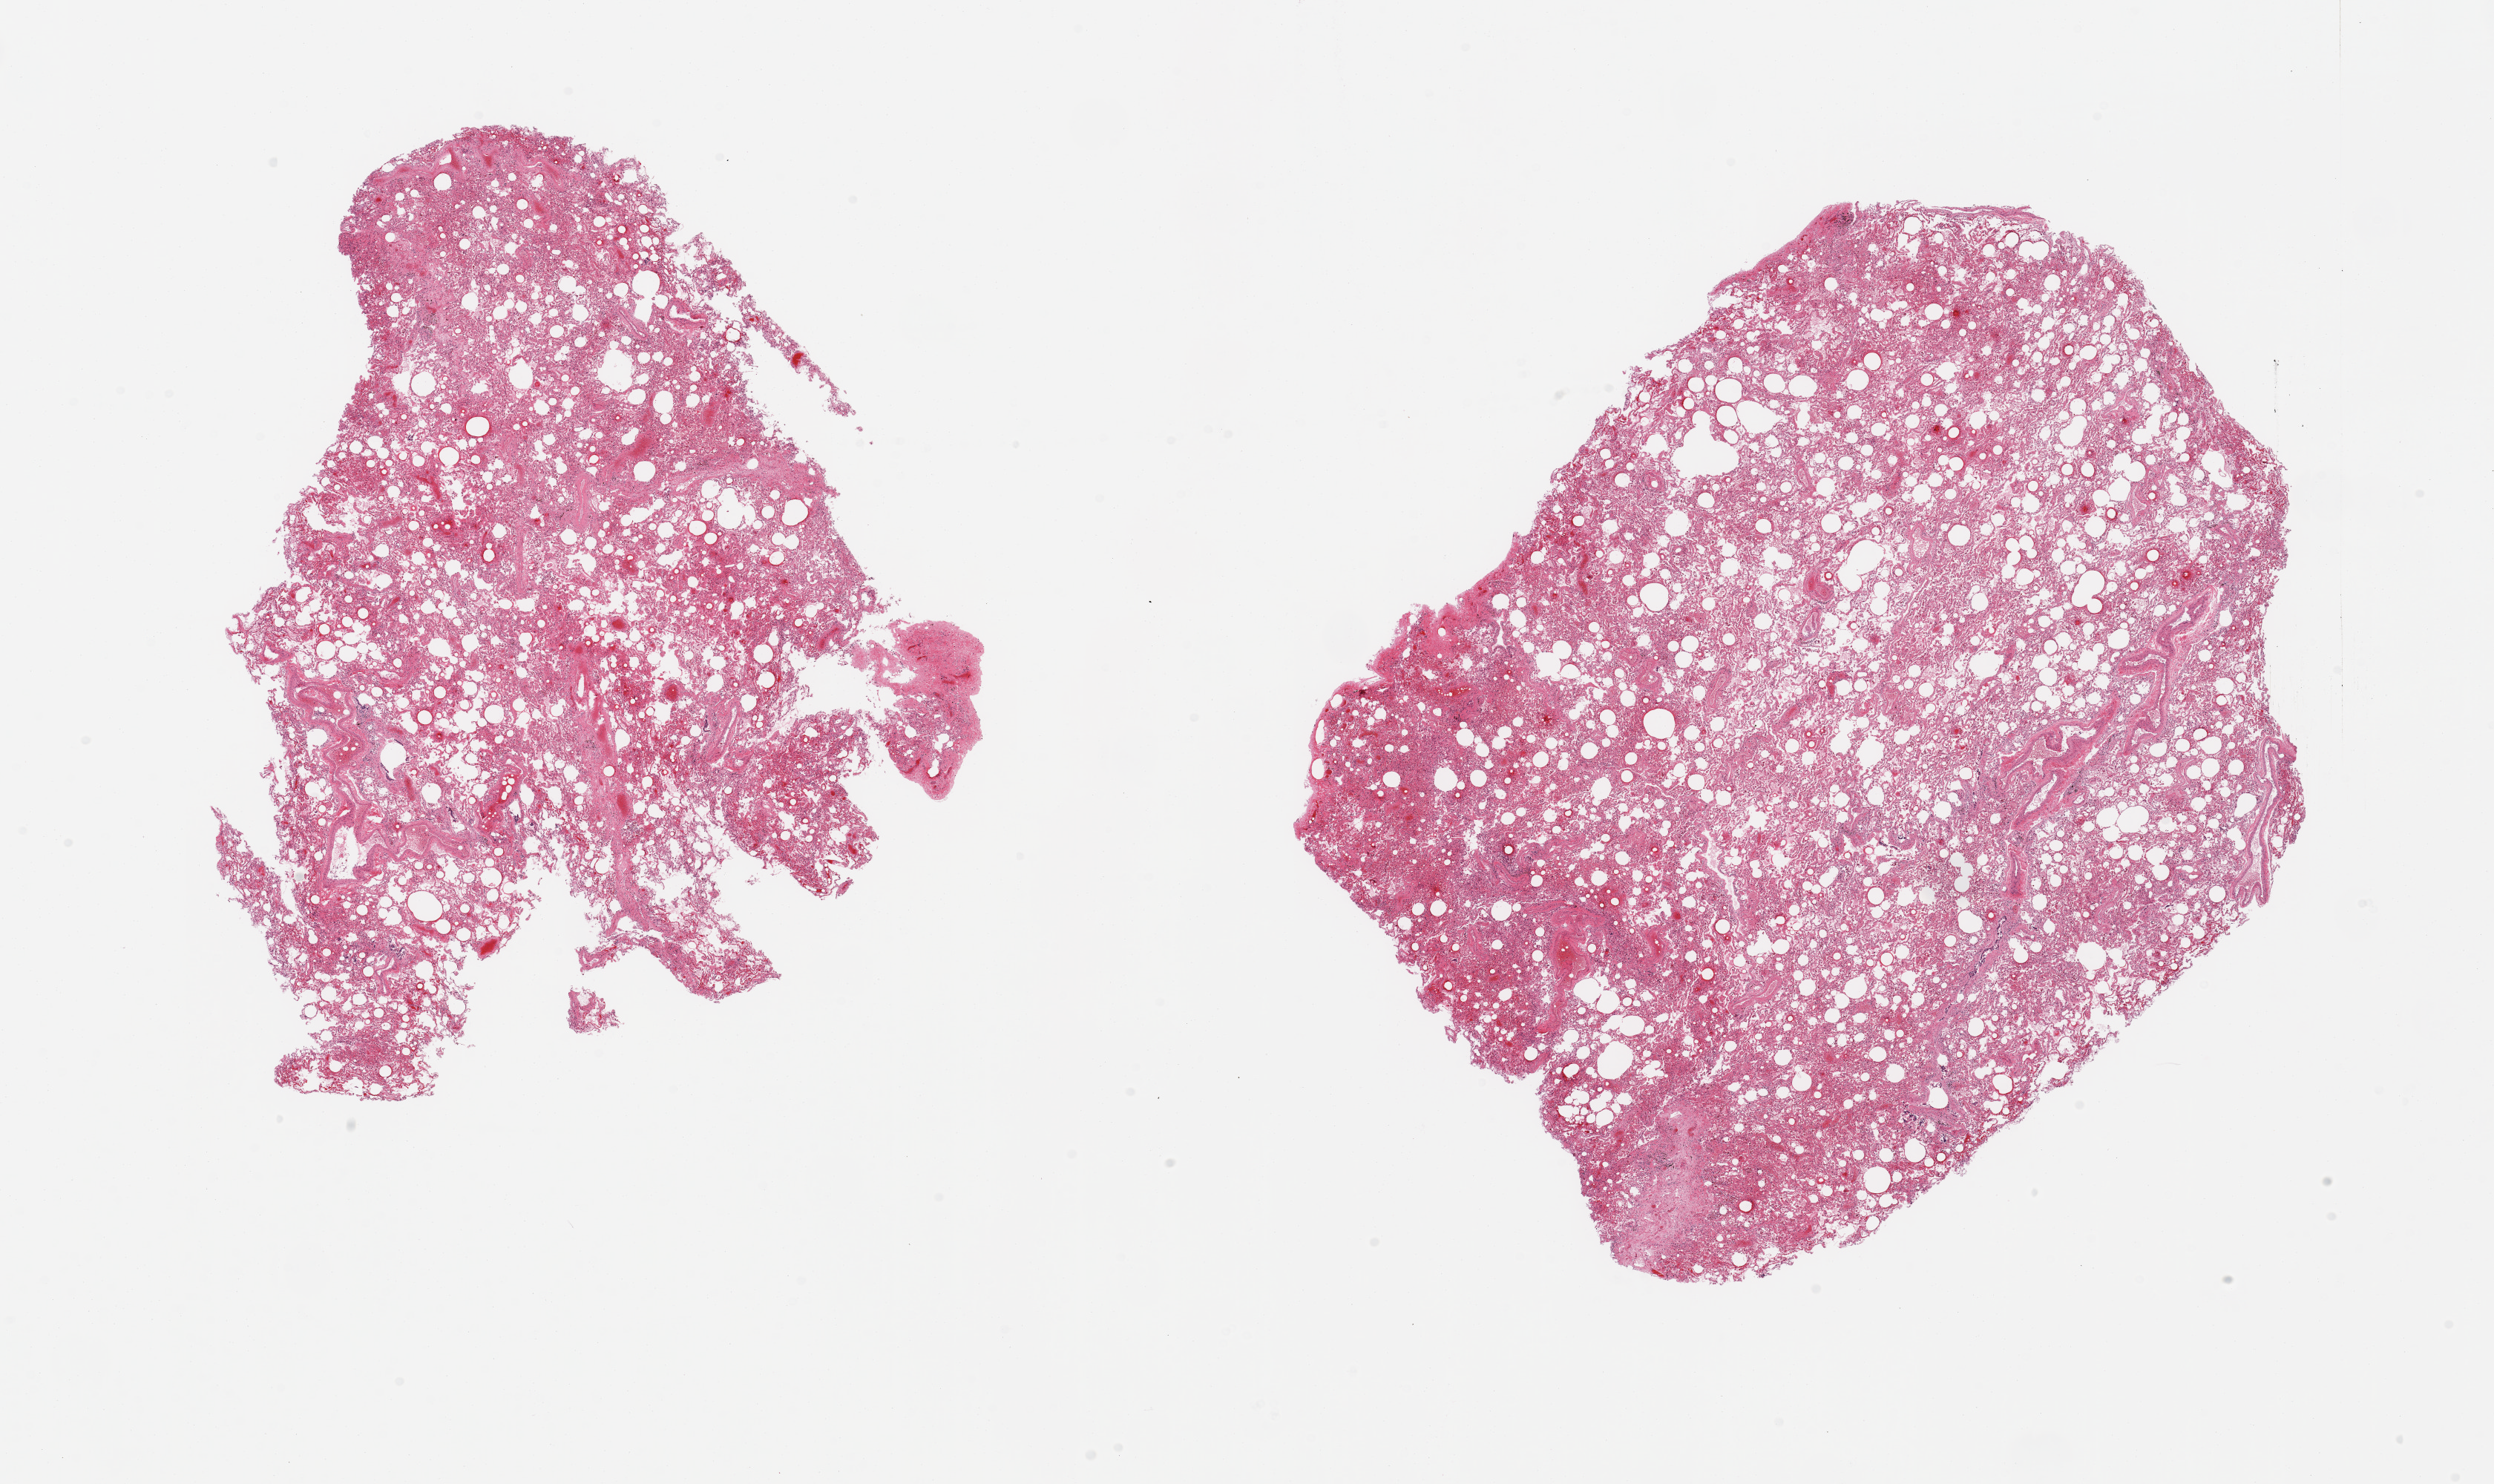
Digitized haematoxylin and eosin-stained section — a low-resolution overview of the entire scanned area, about 26.6 x 15.8 mm (acquisition: 20x scan); PAXgene-fixed paraffin-embedded (PFPE) section; target tissue: lung; tissue donor sample. Male donor.
- pathologist's review note for this sample: 2 pieces; foci of alveolar macrophages